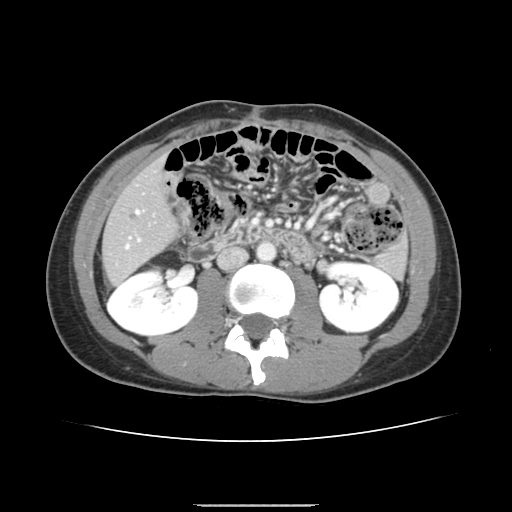
Contrast-enhanced abdominal CT, one axial slice. Slice 53 of 150 in the series (ordered by position). 120 kVp. Intravenous contrast given. Soft-tissue window (W 400 / L 40 HU). 2.5 mm slice thickness. 512 × 512 image matrix, field of view 324 × 324 mm. Female patient, age 32 years. Case-level facts recorded for this patient, not image findings: diagnosis: colorectal cancer liver metastases, imaged before liver resection; multiple liver metastases: yes; largest metastasis: 0.7 cm; chemotherapy before resection: yes.
Structures marked on this image (outlined manually by an expert reader):
- hepatic veins: box from (x=126, y=210) to (x=139, y=248) px
- liver: (x=103, y=163)–(x=176, y=283)
- planned liver remnant (the part of the liver to remain after resection): (x=104, y=161)–(x=175, y=284)
- portal vein (with intrahepatic branches): (x=138, y=239)–(x=140, y=241)